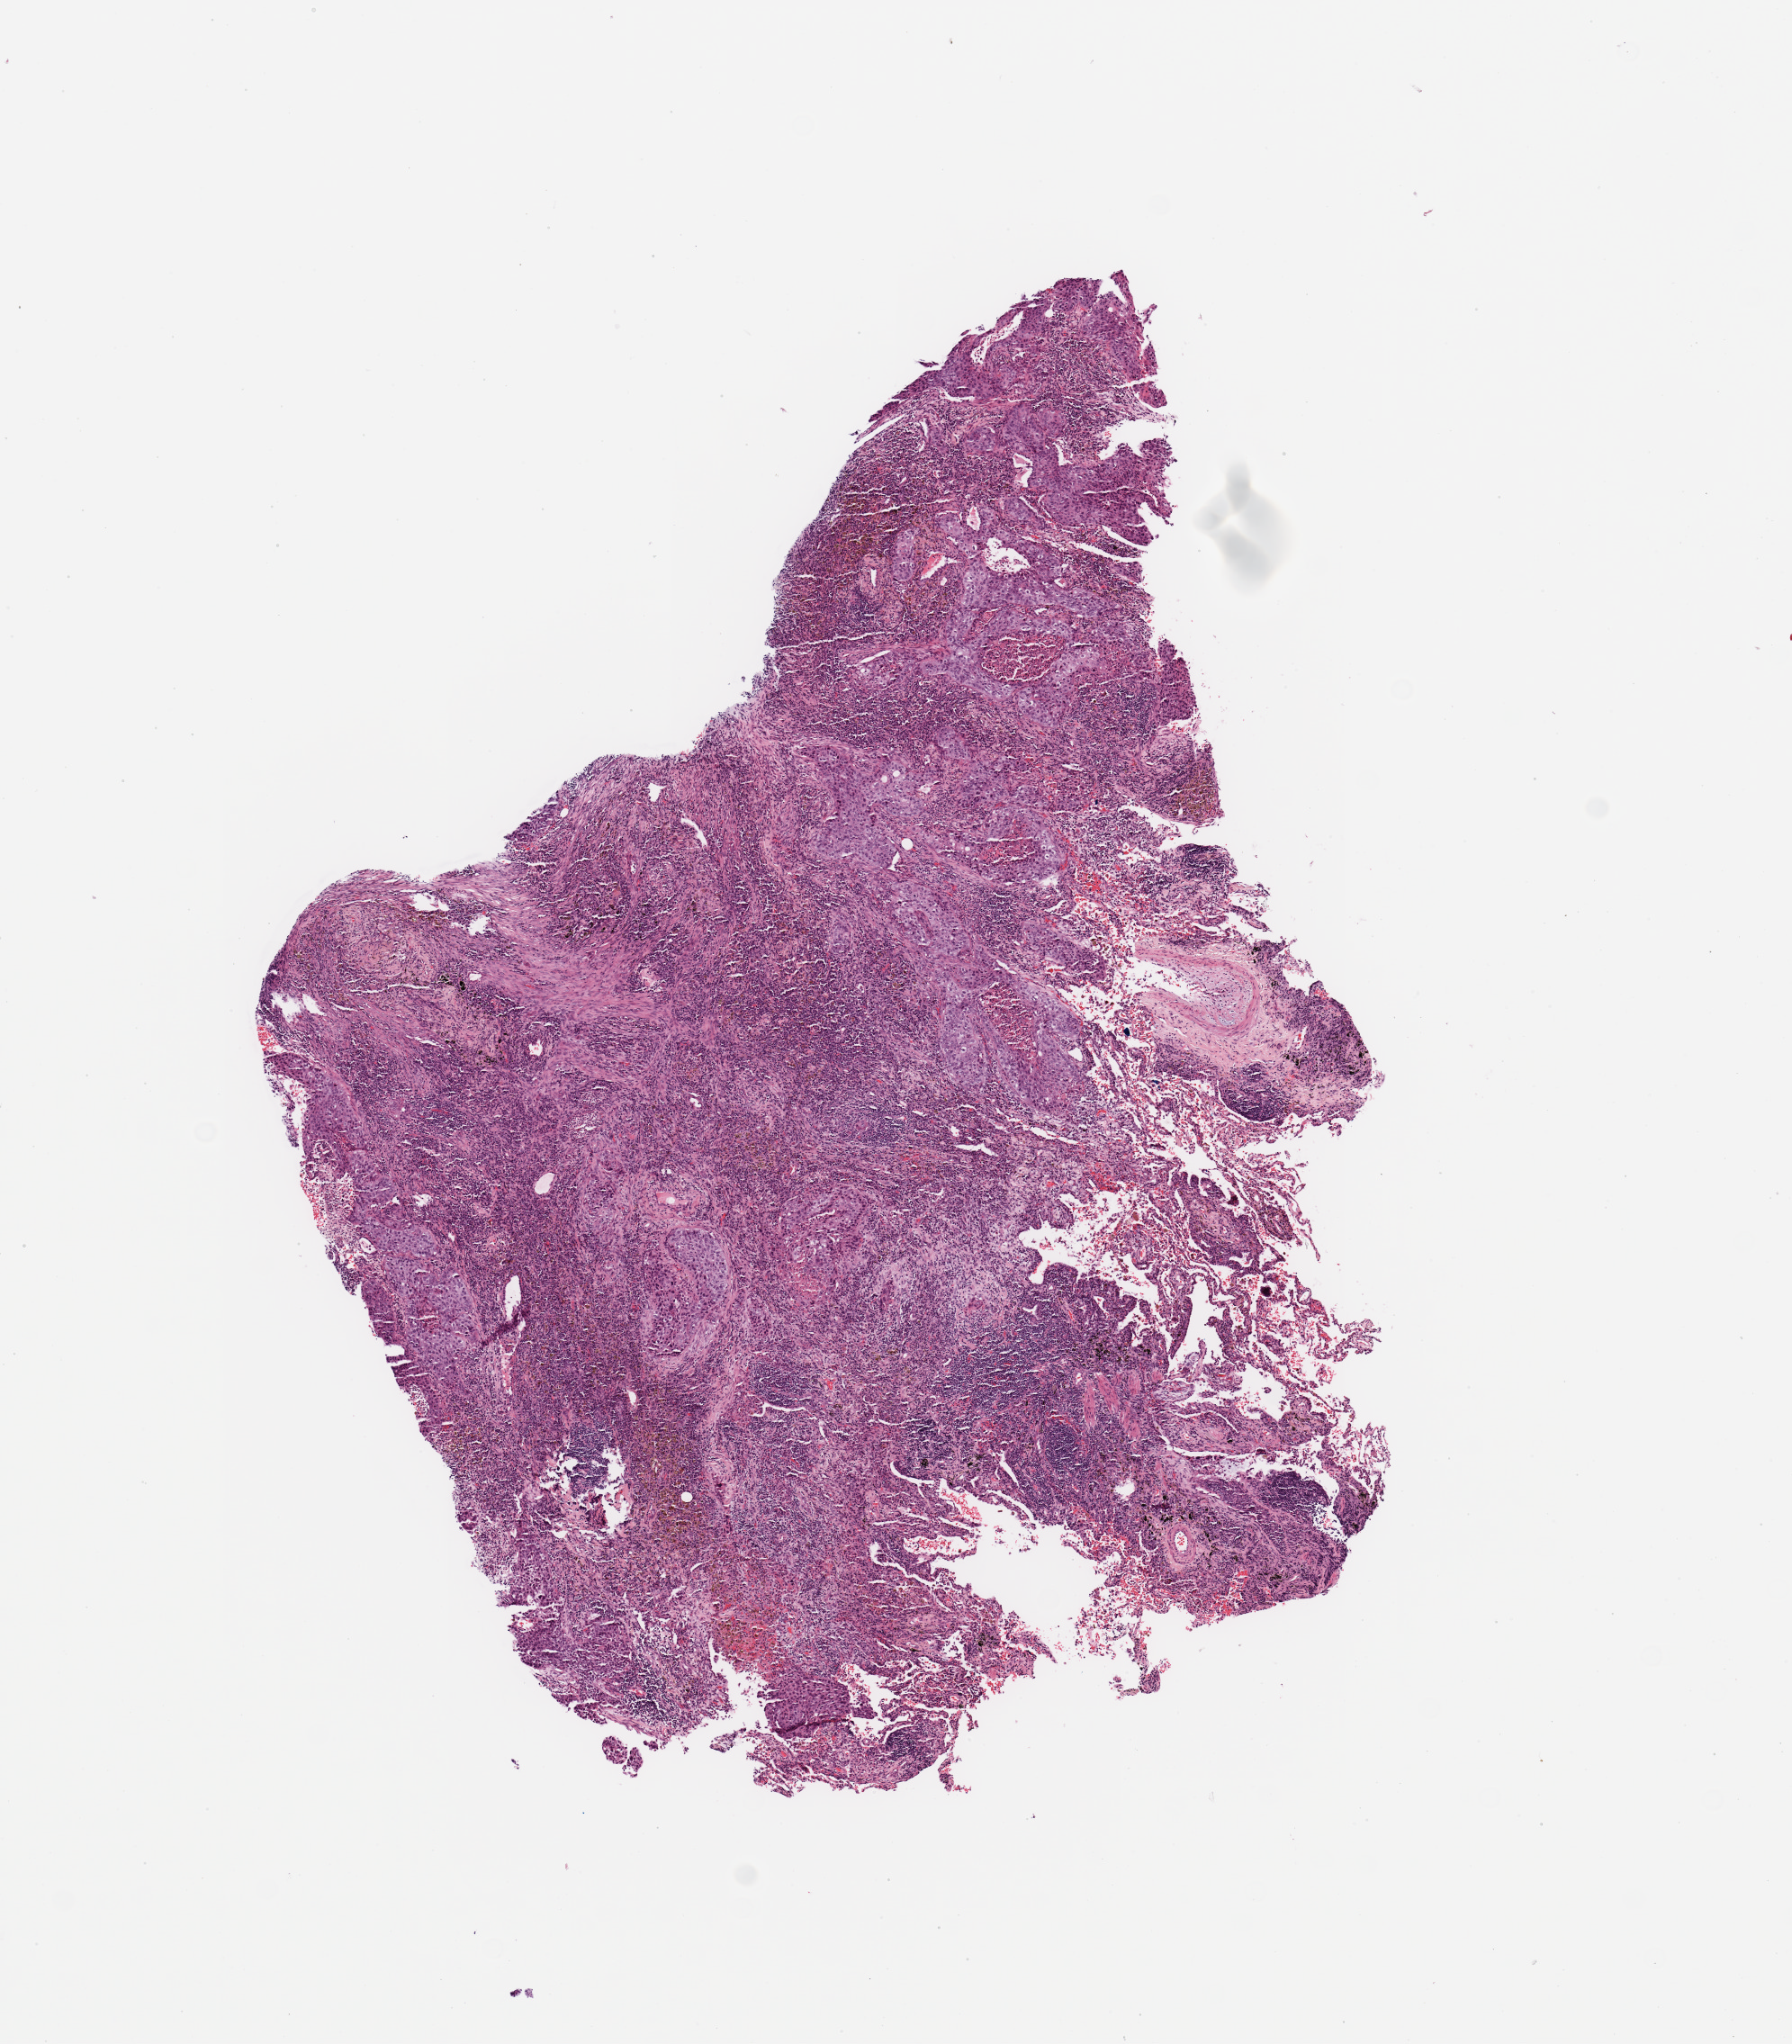
Digitized H&E-stained tissue section (whole slide) — a low-resolution overview of the entire scanned area, about 7.9 x 9.0 mm (from a 20x scan); tumour tissue sample, sampled site: lung. 71-year-old male patient. Histologic grade: G2 (moderately differentiated). Pathologist review of this section (percent, as recorded): tumour nuclei 75%, necrosis 2%.
- AJCC pathologic stage: I
- primary tumour site (as recorded): left lower lobe
- histologic diagnosis: Squamous cell carcinoma, NOS